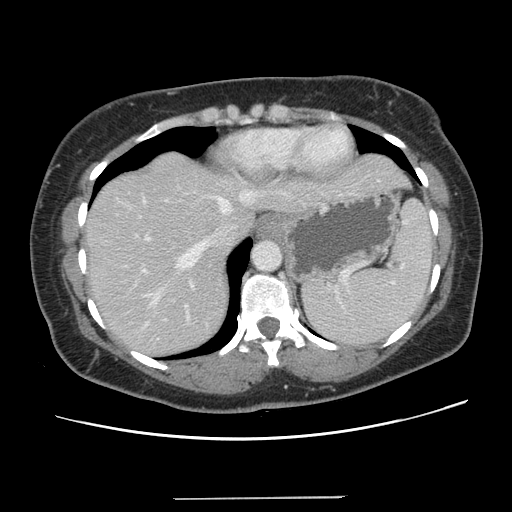
Contrast-enhanced abdominal CT, one axial slice; position 108 of 141 along the scan axis; 120 kVp; intravenous contrast given; soft-tissue window (W 400 / L 40 HU); 2.5 mm slice thickness; 512 × 512 image matrix. Female patient, age 53 years. Case-level facts recorded for this patient, not image findings: diagnosis: colorectal cancer liver metastases, imaged before liver resection; multiple liver metastases: no; largest metastasis: 14.5 cm.
Outlined on this slice (expert manual segmentation):
- hepatic veins: bounding box [x1, y1, x2, y2] px = [113, 188, 287, 305]
- liver: [85, 152, 409, 358]
- planned liver remnant (the part of the liver to remain after resection): [85, 208, 256, 358]
- portal vein (with intrahepatic branches): [139, 199, 190, 322]